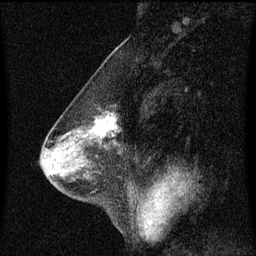
Breast MRI (dynamic contrast-enhanced), one sagittal slice; slice 31 of 60 in the series (ordered by position); dynamic contrast-enhanced series, image 2 of 3 at this slice position (ordered by acquisition); 1.5 T; TE 4.2 ms, TR 8.4 ms; 2 mm slice thickness; 256 × 256 image matrix, field of view 200 × 200 mm. Patient: female, 58 years.
Annotated regions visible in this slice (semi-automatically segmented with operator editing):
- analysis volume of interest (the breast-tissue region the enhancement analysis was run in; not a lesion): bounding box [x1, y1, x2, y2] px = [79, 106, 122, 143]
- tumour enhancement mask (voxels above the 70 % enhancement threshold inside the analysis volume of interest): [92, 116, 118, 139]